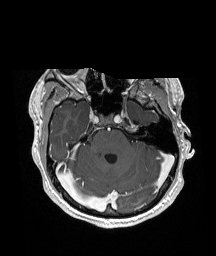
Brain MRI from a brain-tumour surgery series, one axial slice. Position 125 of 192 along the scan axis. T1-weighted post-contrast. 216 × 256 image matrix, field of view 211 × 250 mm. Case-level facts recorded for this patient, not image findings: histopathology: Glioneuronal tumor; WHO grade: 2; tumour location: Left Superior Temporal Gyrus.
Outlined on this slice (outlined manually by an expert reader):
- previous resection cavity: bounding box [x1, y1, x2, y2] px = [135, 122, 138, 124]